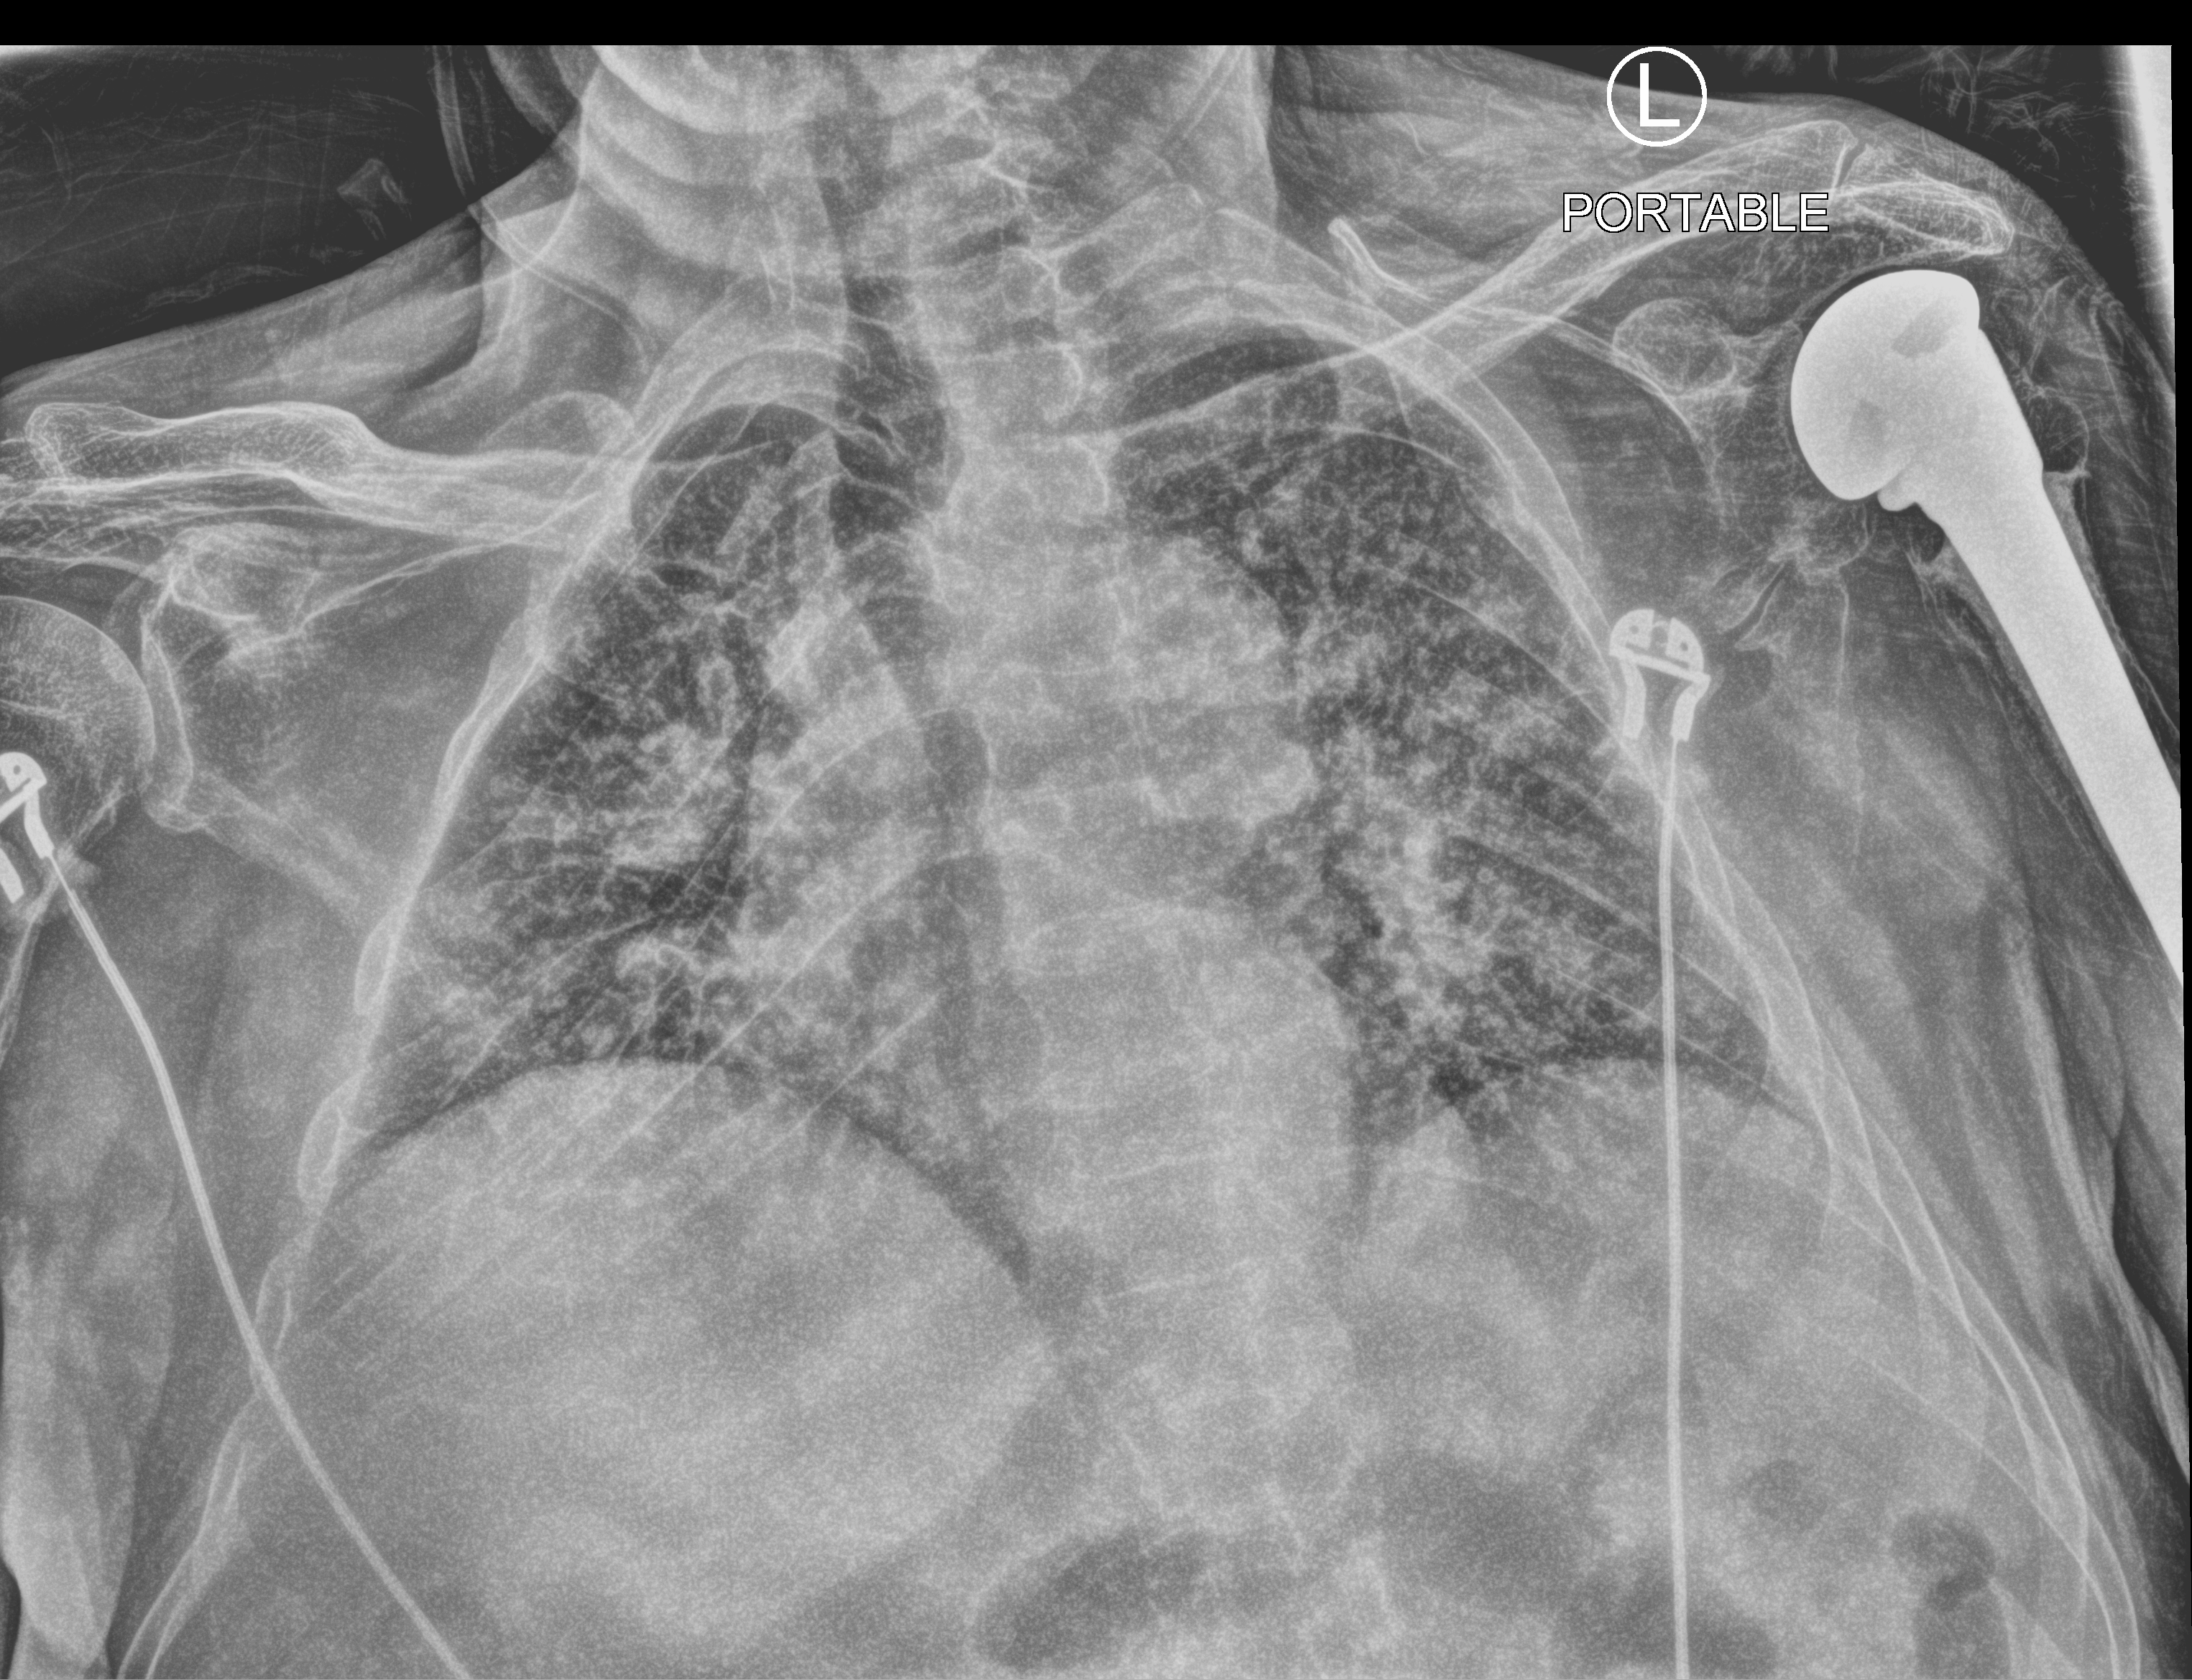
Chest X-ray (portable), anteroposterior (AP) projection. Male patient hospitalised with COVID-19, age 60–74 years.
Admission-level facts for this patient (not findings on this image; timing relative to this image not recorded): admitted to intensive care during this hospital stay: no; chronic kidney disease (admission record): no; length of hospital stay: 10 days.